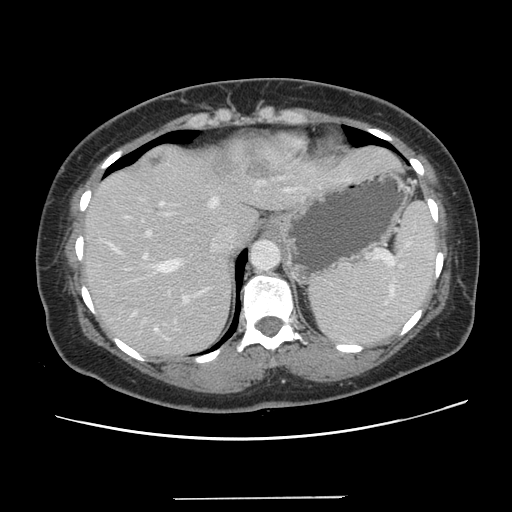
Contrast-enhanced abdominal CT, one axial slice; slice 101 of 141 in the series (ordered by position); intravenous contrast given; soft-tissue window (W 400 / L 40 HU); 512 × 512 image matrix, field of view 366 × 366 mm. Female patient, age 53 years. From the clinical record (not read from this slice): diagnosis: colorectal cancer liver metastases, imaged before liver resection; multiple liver metastases: no; largest metastasis: 14.5 cm.
Annotated regions visible in this slice (outlined manually by an expert reader):
- hepatic veins: bounding box <117,177,284,331> (left, top, right, bottom; pixels)
- liver: <84,143,399,357>
- planned liver remnant (the part of the liver to remain after resection): <84,209,260,357>
- portal vein (with intrahepatic branches): <124,189,288,322>
- liver metastasis: <148,156,163,168>
- liver metastasis: <209,147,273,180>